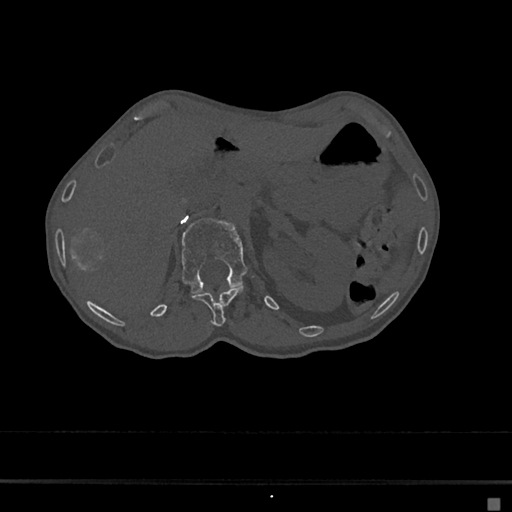
CT including the spine, one axial slice. Reconstruction kernel Br40s/3. 120 kVp. Bone window (W 1800 / L 400 HU). 0.5 mm slice thickness. 512 × 512 image matrix. Female patient, age 68 years. Case-level facts recorded for this patient, not image findings: primary cancer: renal.
Structures marked on this image (semi-automatic segmentation, software-assisted and operator-edited):
- L1 vertebra: bounding box (x1, y1, x2, y2) in pixels: (181, 218, 248, 294)
- T12 vertebra: (192, 287, 244, 327)